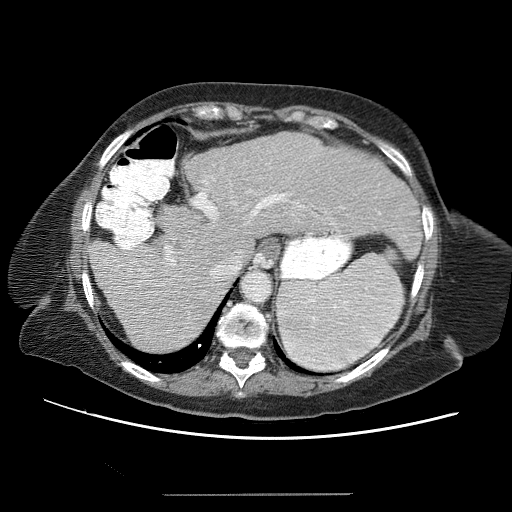
Contrast-enhanced abdominal CT (liver protocol), one axial slice. Slice 45 of 65 in the series (ordered by position). Reconstruction kernel STANDARD. 120 kVp. Soft-tissue window (W 400 / L 40 HU). 2.5 mm slice thickness. 512 × 512 image matrix. From the clinical record (not read from this slice): diagnosis: hepatocellular carcinoma (patient treated with transarterial chemoembolisation; whether this scan precedes or follows treatment is not stated here); TNM stage (as recorded): Stage-IIIB; Child-Pugh class: A; tumour differentiation: moderately differentiated; tumour nodularity: uninodular.
Outlined on this slice (semi-automatic segmentation, software-assisted and operator-edited):
- liver parenchyma outside the tumour (the mass and vessels are separate outlines, so this box may not span the whole liver): bounding box <88,132,423,348> (left, top, right, bottom; pixels)
- mass: <156,245,181,270>
- liver vessels: <117,152,414,333>